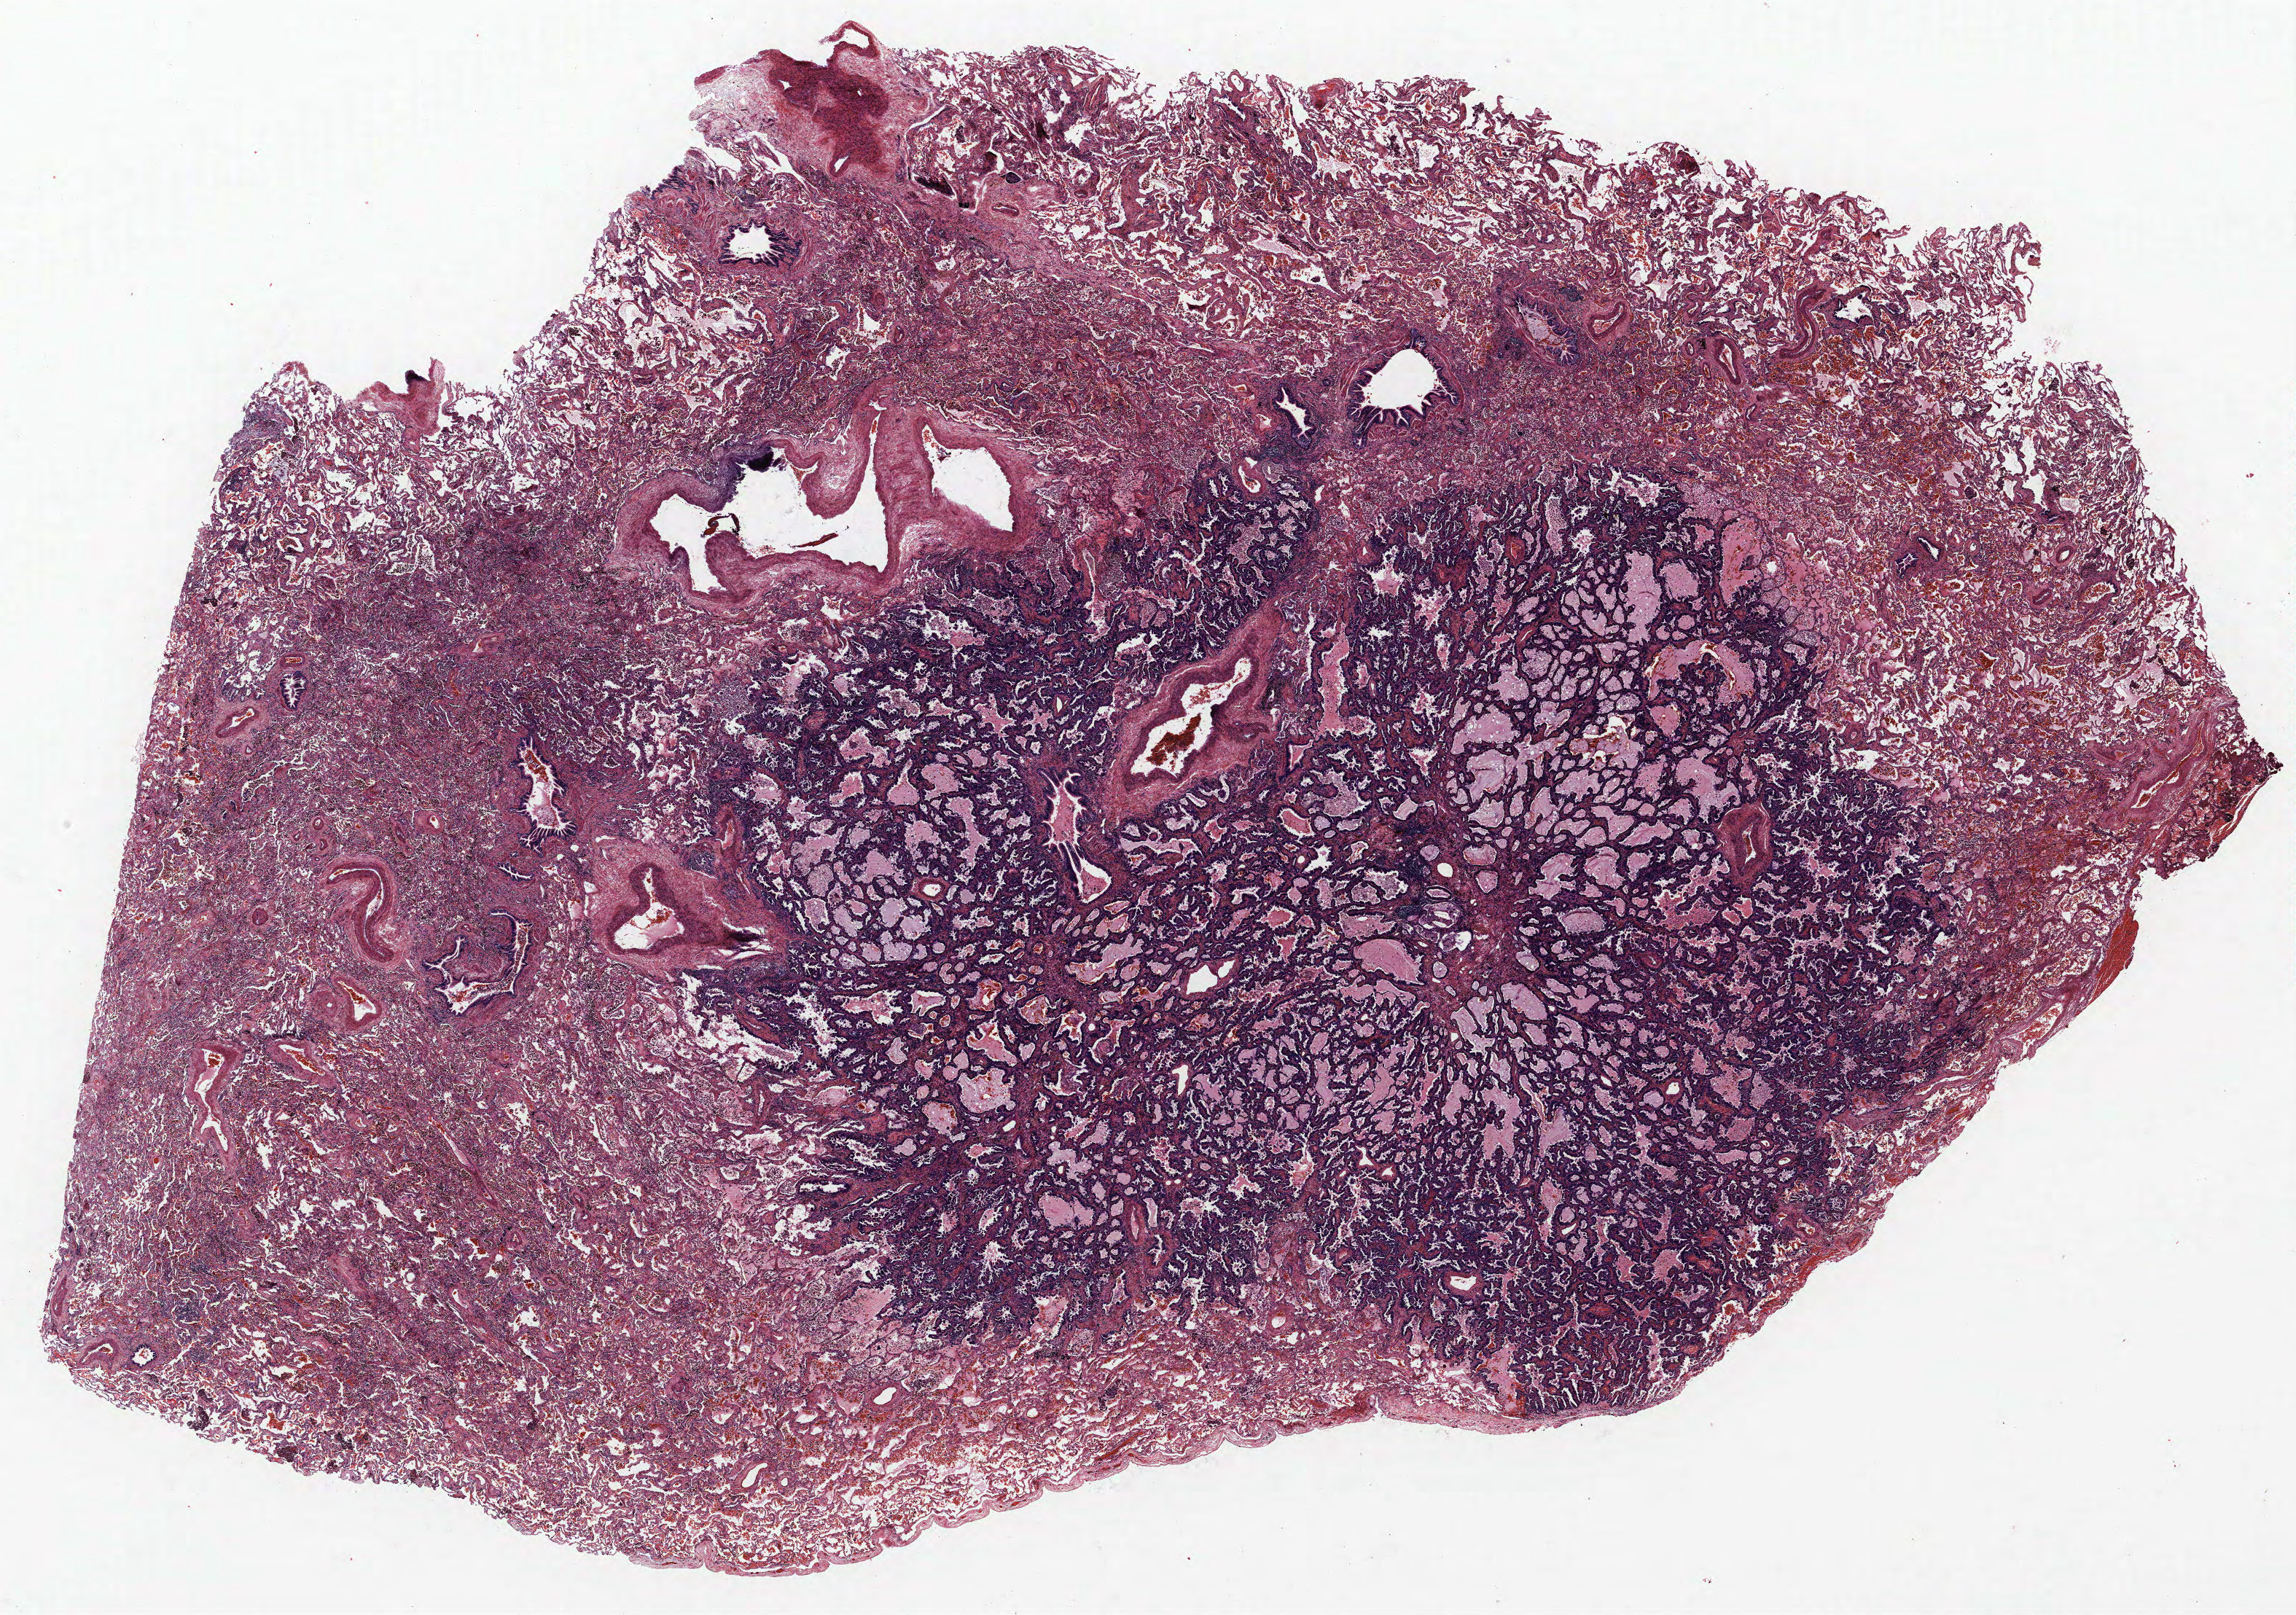
Whole-slide histology image, Hematoxylin and eosin (H&E) stained, low-resolution overview of the scanned area, about 25.2 x 17.7 mm (slide scanned at 40x), FFPE section, lung. Female, age 55 at enrolment. Current smoker at enrolment.
Participant's lung-cancer diagnosis: Bronchiolo-alveolar adenocarcinoma, NOS (ICD-O-3 8250/3).